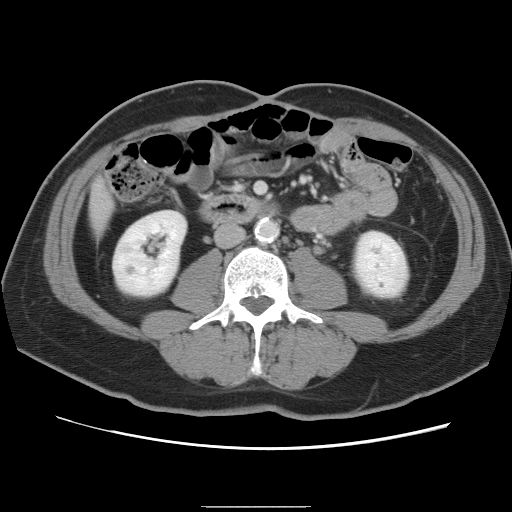
Contrast-enhanced abdominal CT, one axial slice; position 17 of 87 along the scan axis; 120 kVp; intravenous contrast given; soft-tissue window (W 400 / L 40 HU); 5 mm slice thickness; 512 × 512 image matrix, field of view 363 × 363 mm. Male patient, age 63 years. Case-level facts recorded for this patient, not image findings: diagnosis: colorectal cancer liver metastases, imaged before liver resection; multiple liver metastases: no; largest metastasis: 9 cm.
Annotated regions visible in this slice (expert manual segmentation):
- liver: box from (x=90, y=180) to (x=114, y=228) px
- planned liver remnant (the part of the liver to remain after resection): (x=90, y=181)–(x=113, y=228)